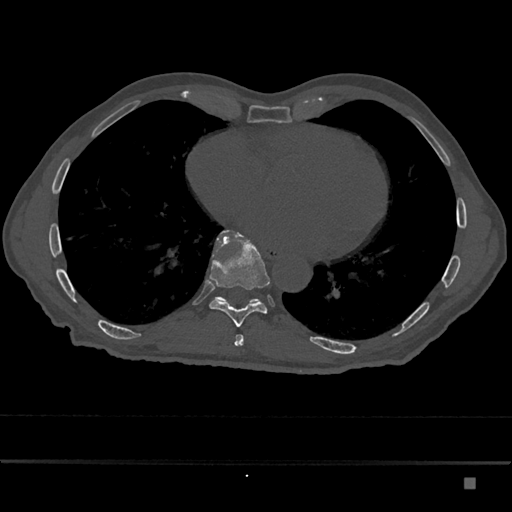
CT including the spine, one axial slice; slice 793 of 797 in the series (ordered by position); reconstruction kernel Br40s/3; 120 kVp; bone window (W 1800 / L 400 HU); 0.5 mm slice thickness; 512 × 512 image matrix, field of view 390 × 390 mm. Patient: male, 72 years. Case-level facts recorded for this patient, not image findings: primary cancer: prostate.
Outlined on this slice (semi-automatically segmented with operator editing):
- T10 vertebra: bounding box [x1, y1, x2, y2] px = [215, 231, 261, 303]
- T9 vertebra: [209, 230, 270, 328]